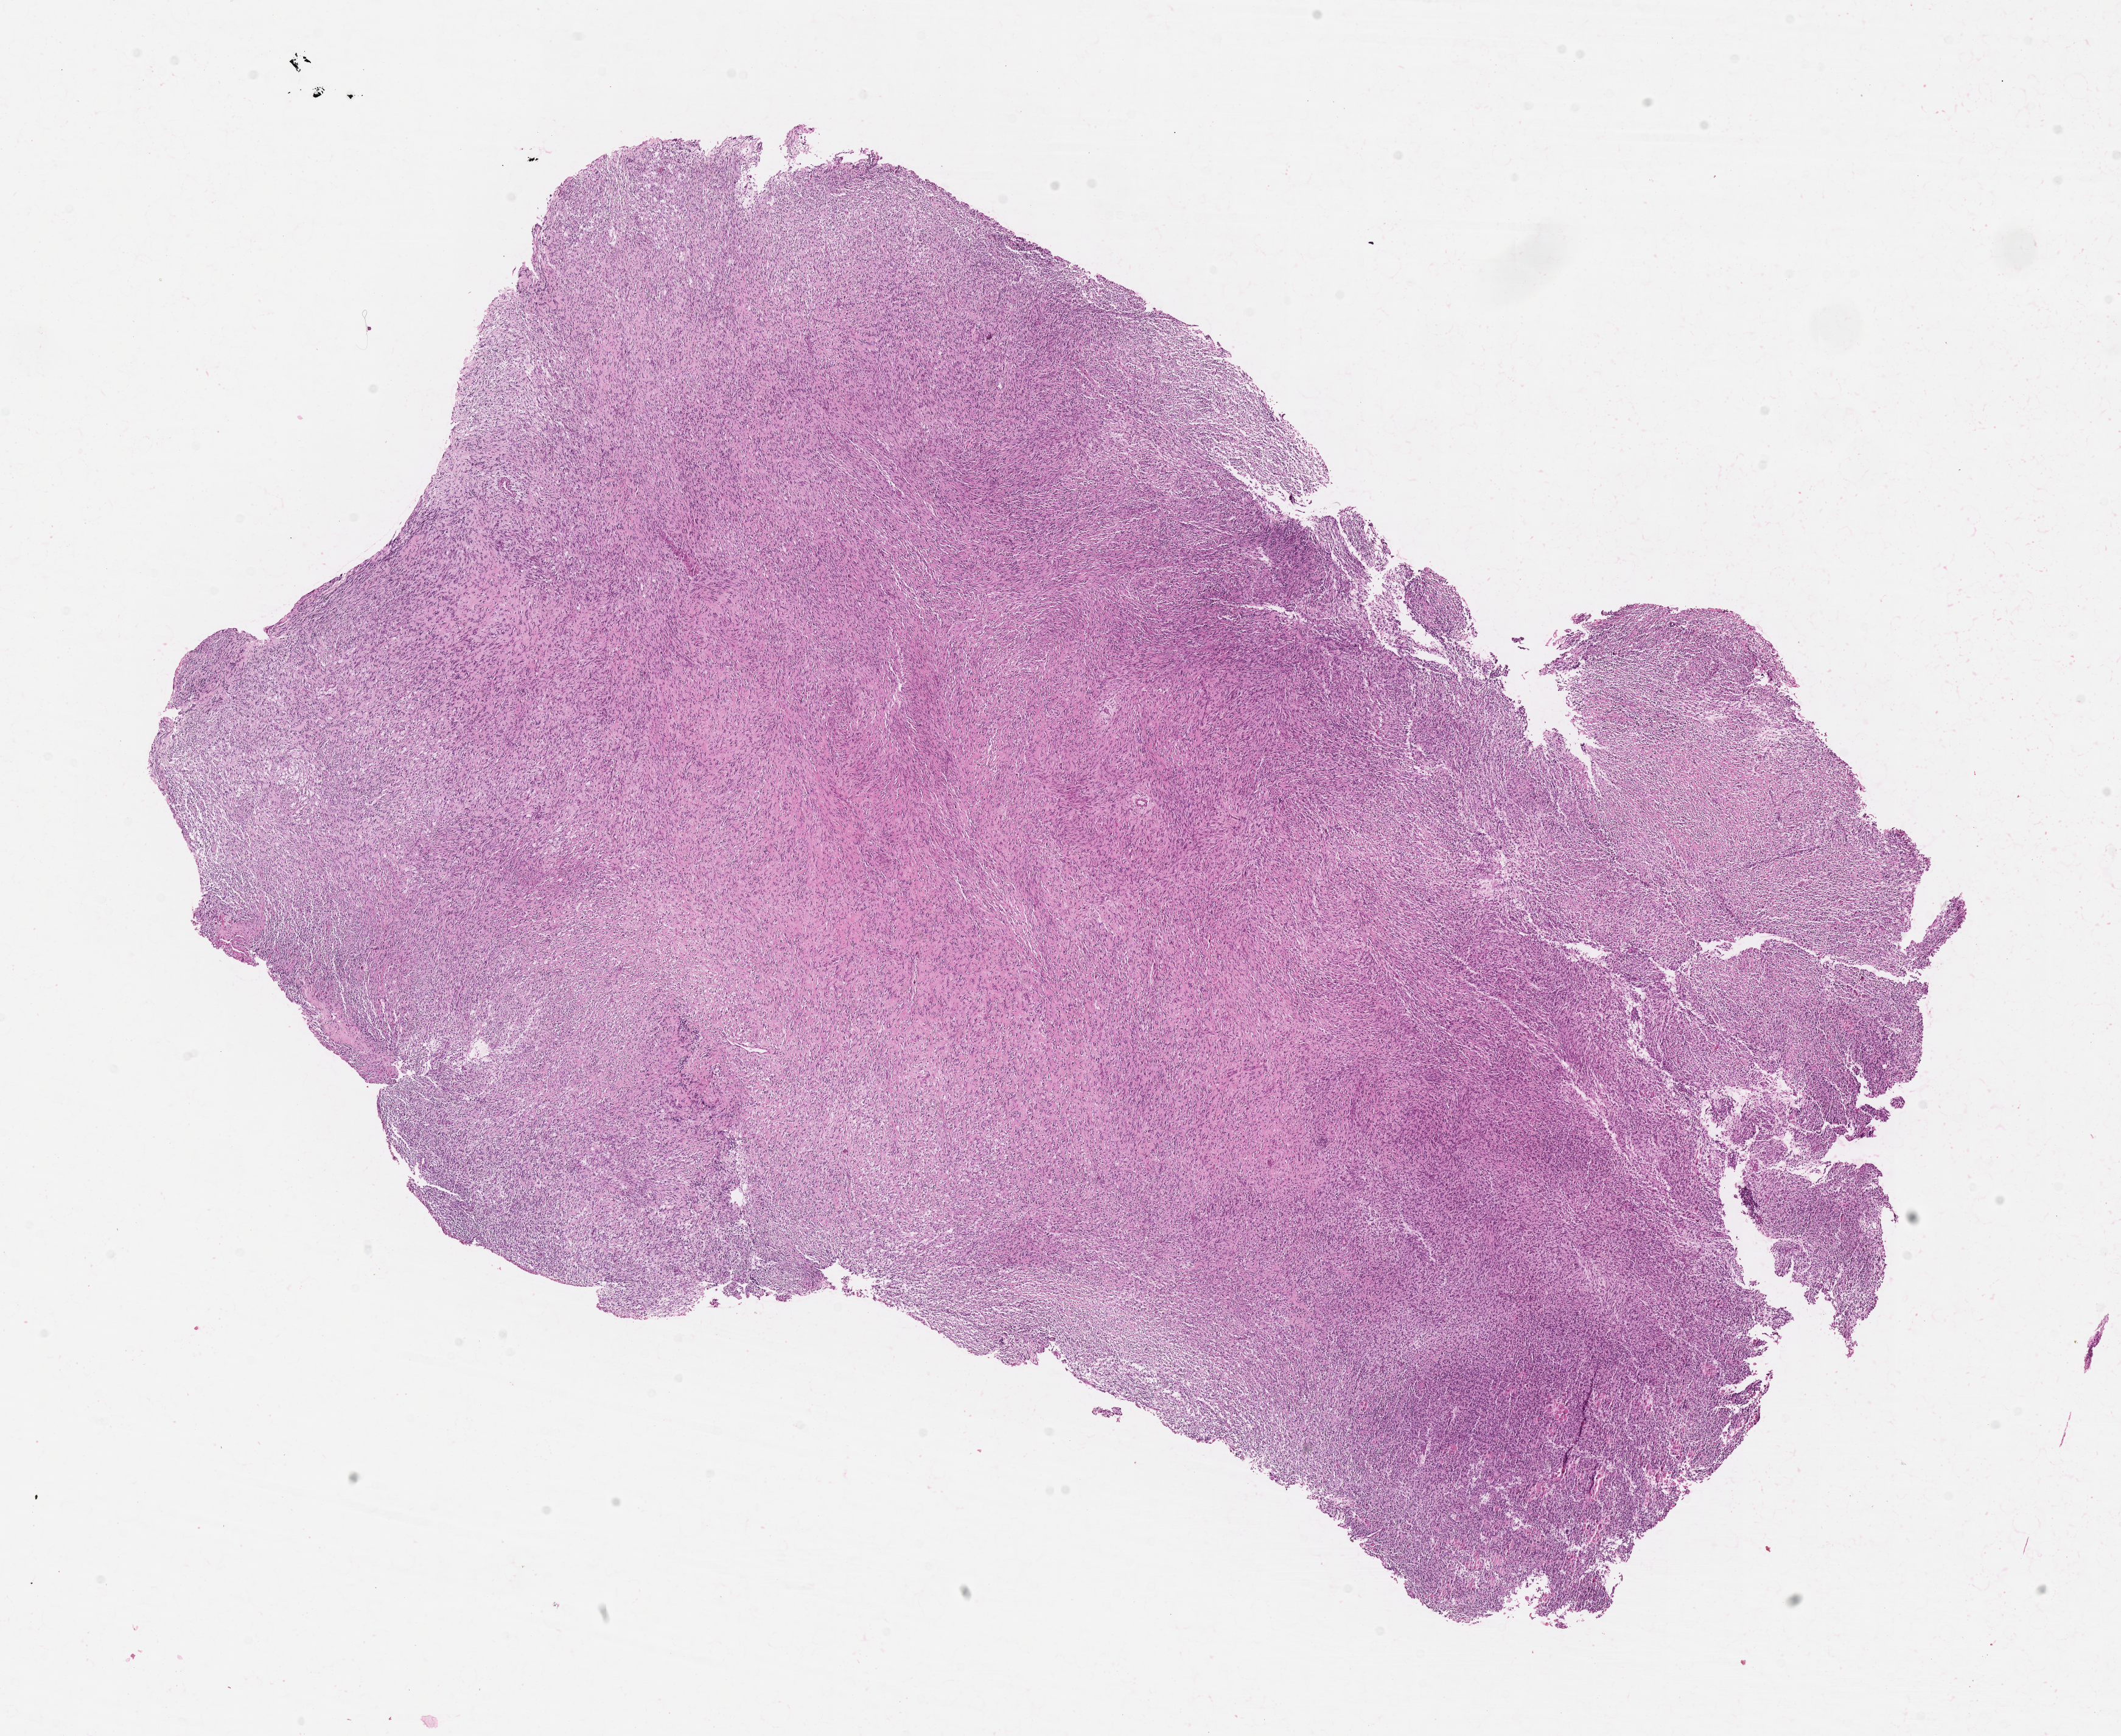
Digitized hematoxylin and eosin (H&E)-stained section of tumor tissue — shown as a low-resolution overview of the whole scanned area (about 14.1 x 11.5 mm); formalin-fixed paraffin-embedded section; sample anatomic site: bone, temporal-infra (infratemporal fossa). Patient: female, age 14.4 years at diagnosis.
Diagnosis: rhabdomyosarcoma; histological classification: embryonal rhabdomyosarcoma. Stage (as recorded): 3.